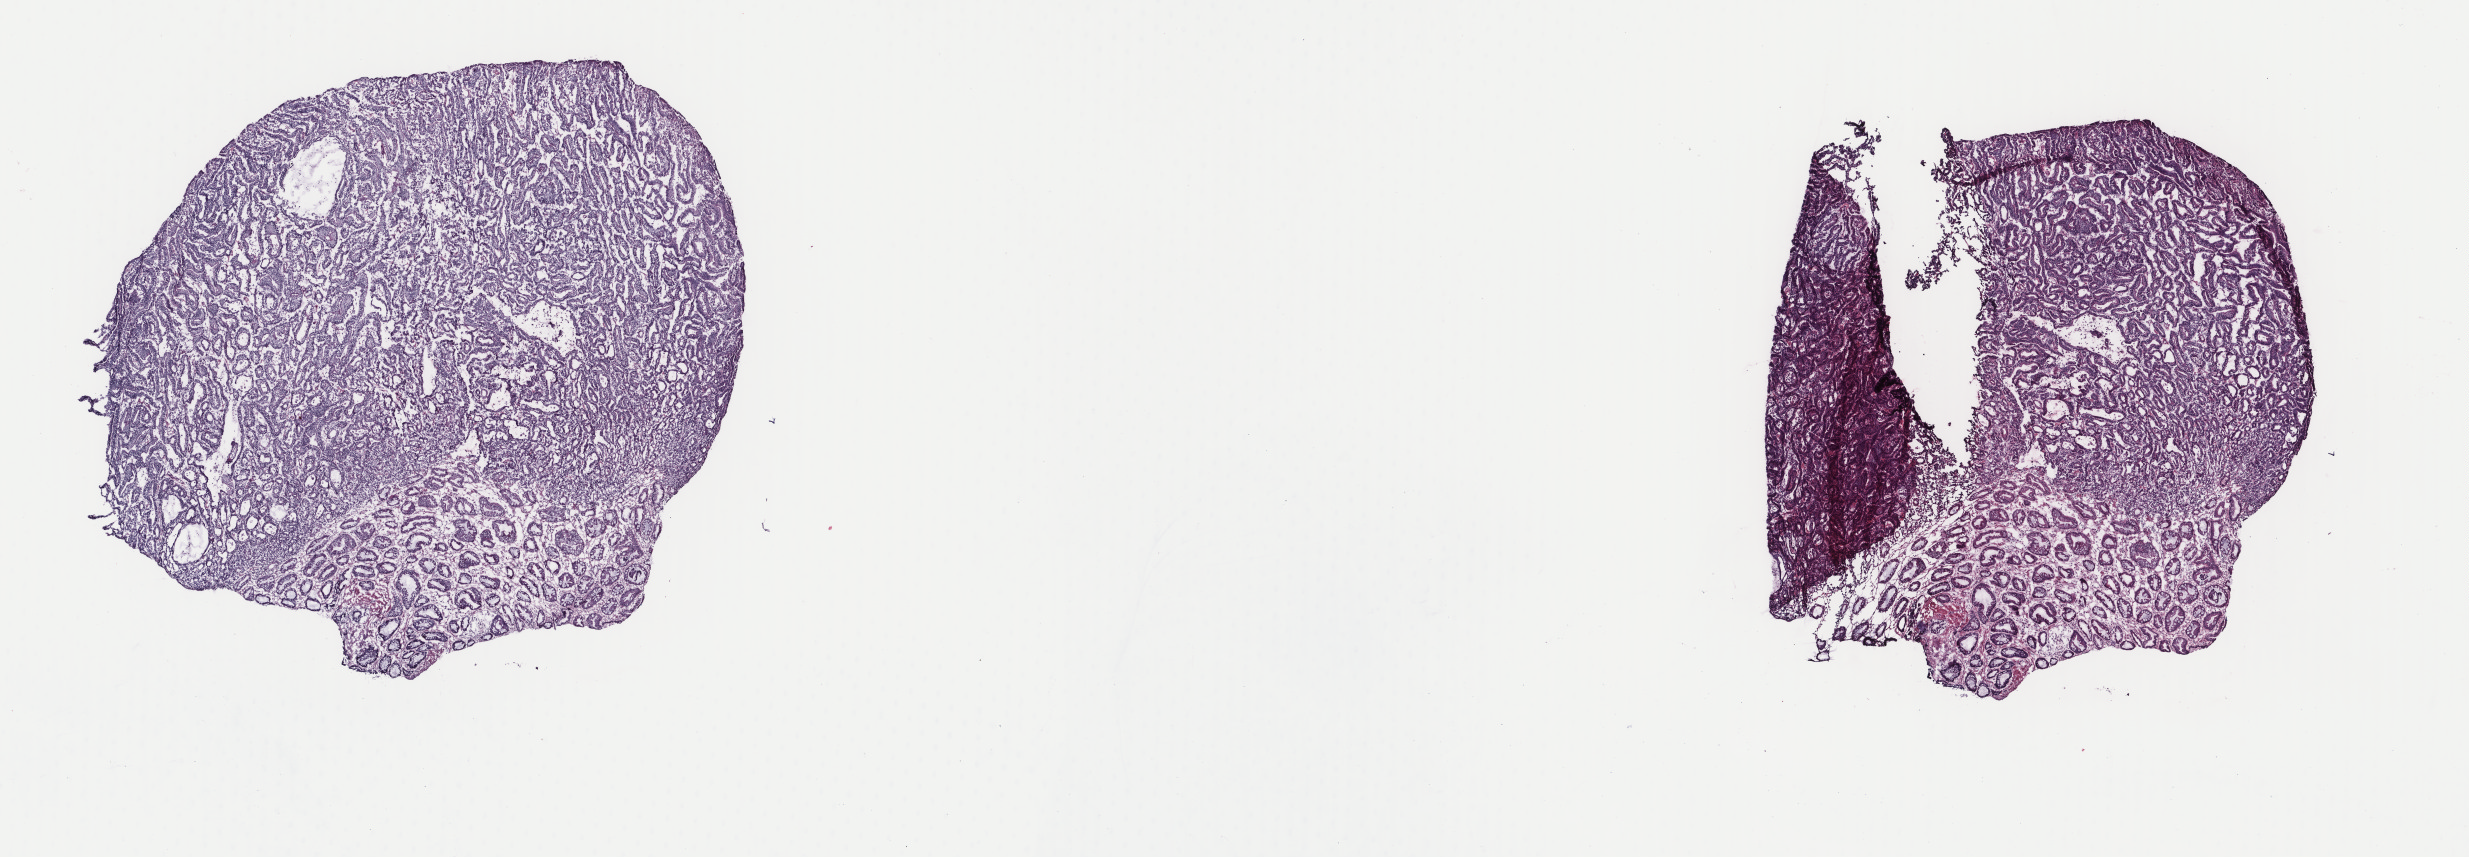
Hematoxylin and eosin (H&E) stained whole-slide image — low-resolution overview of the scanned area, about 19.6 x 6.8 mm (from a 40x scan); frozen section from the top of the tissue portion; sample: primary tumour, stomach. Male patient; age at initial diagnosis 77 years. Histologic grade: G2 (moderately differentiated). Slide review estimates, as recorded: tumour cells 80%, tumour nuclei 75%, normal cells 20%, stromal cells 0%, necrosis 0%. Inflammatory infiltration, as recorded: lymphocyte infiltration 2%, monocyte infiltration 1%, neutrophil infiltration 0%.
AJCC pathologic stage: IB (7th edition). TNM: T1b N1 M0. Lymph nodes positive (case pathology): 1 of 62 examined. Histologic diagnosis: Tubular adenocarcinoma (gastric antrum).